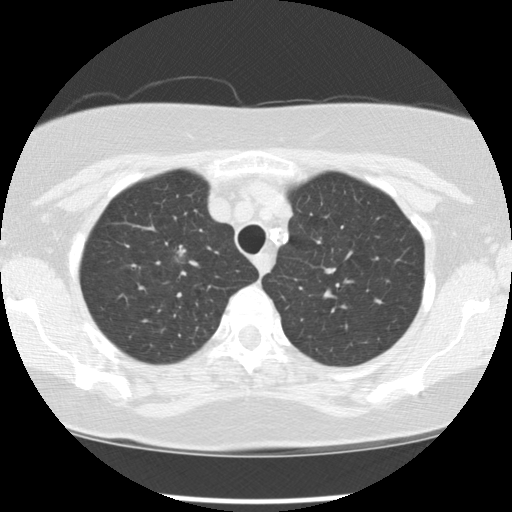
Low-dose screening chest CT, one axial slice; position 91 of 113 along the scan axis; reconstruction kernel STANDARD; 120 kVp; lung window (W 1500 / L -600 HU); 2.5 mm slice thickness; 512 × 512 image matrix, field of view 318 × 318 mm.
Annotated regions visible in this slice (expert manual segmentation):
- lesion 1 (tumor, upper lobe of right lung): bounding box (x1, y1, x2, y2) in pixels: (177, 247, 186, 257)